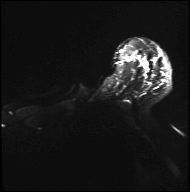
Breast MRI, one axial slice. Slice 30 of 36 in the series (ordered by position). Diffusion-weighted series; image 2 of 4 stored at this slice position (different b-values; order by instance number). 3 T. 4 mm slice thickness. 190 × 192 image matrix, field of view 317 × 320 mm. Female patient.
Annotated regions visible in this slice (expert manual segmentation):
- tumour on diffusion-weighted imaging: bounding box [x1, y1, x2, y2] px = [19, 55, 30, 62]